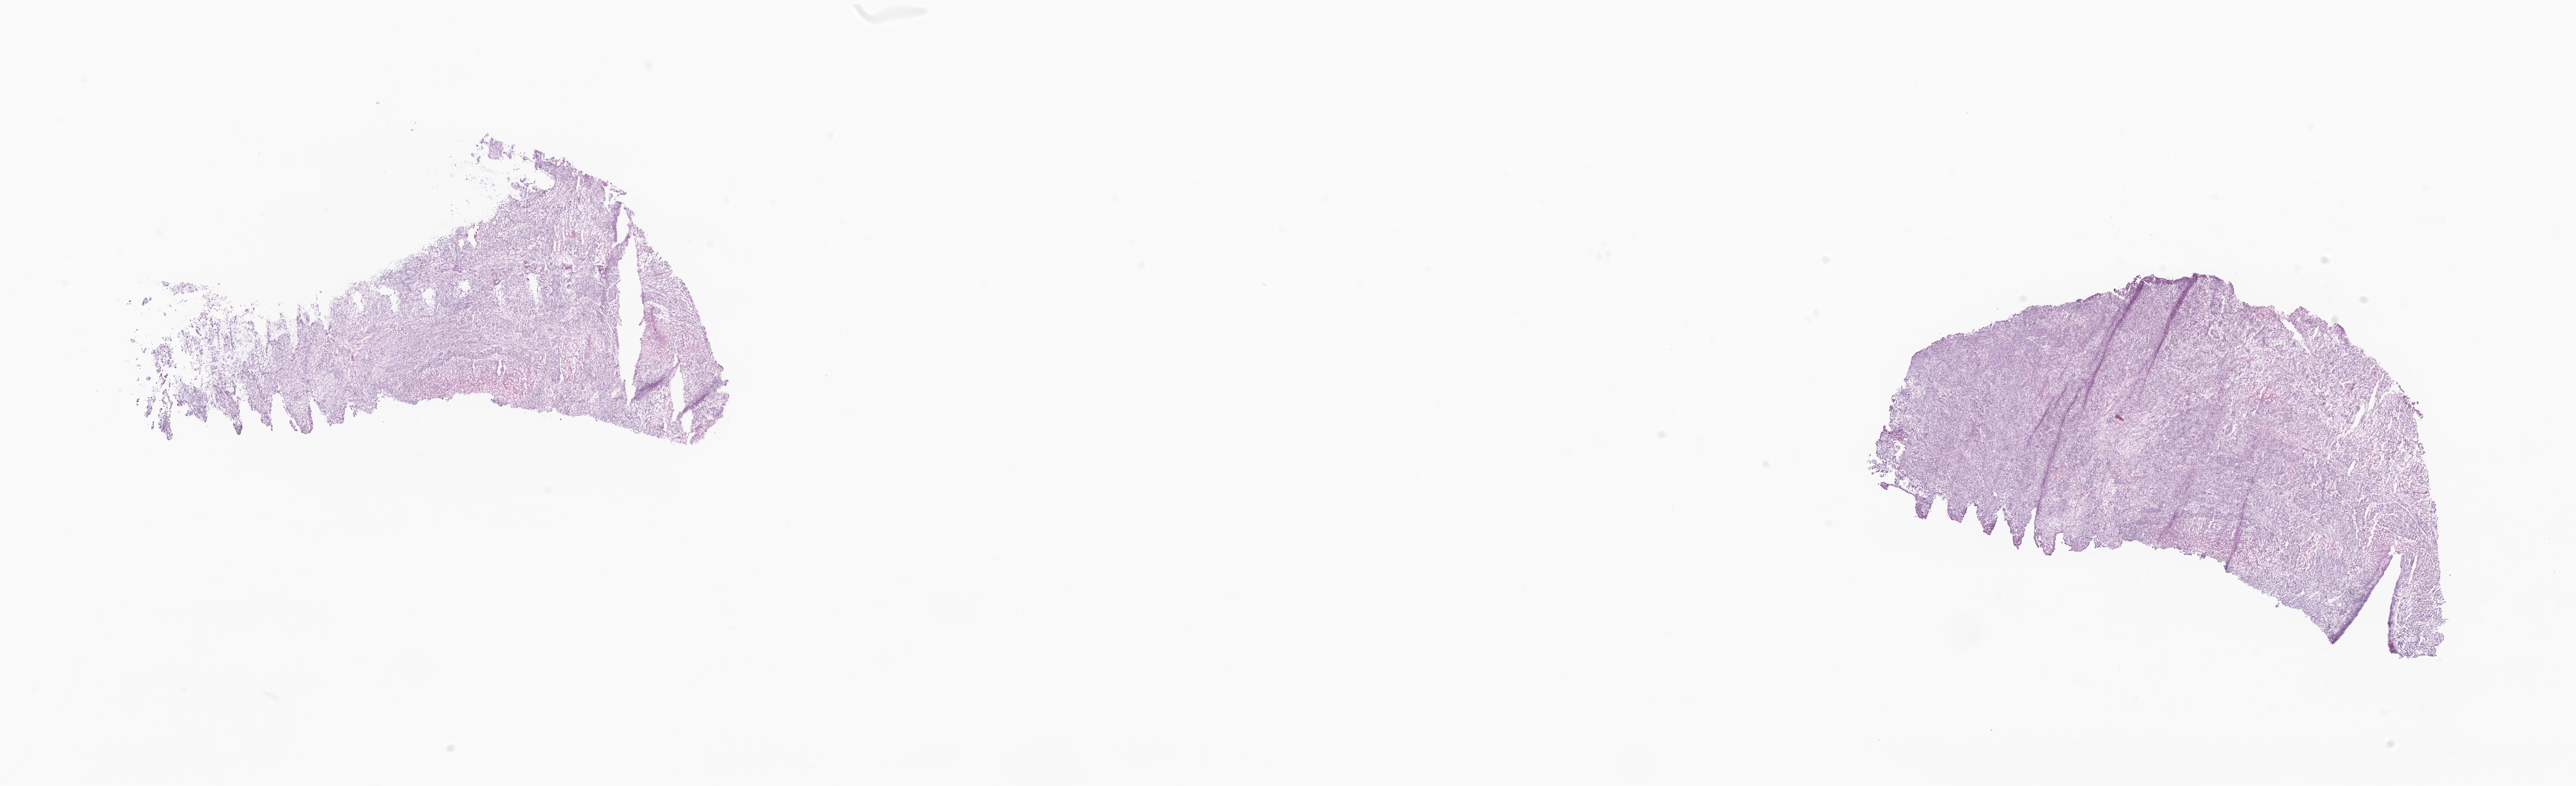
Whole-slide image, hematoxylin and eosin (H&E) stain — shown as a low-resolution overview of the whole scanned area (about 36.9 x 11.3 mm). Frozen section. Metastatic tumor tissue, resected from lymph node. Male, age 58 years at initial diagnosis. Slide review estimates, as recorded: tumor cells 55%, tumor nuclei 71%, stromal cells 16%, necrosis 7%, normal cells 22%. Infiltration values recorded for this section: lymphocyte infiltration 9%, monocyte infiltration 3%, neutrophil infiltration 4%.
* section: bottom of the tissue portion
* patient diagnosis (primary): Adenocarcinoma, metastatic, NOS